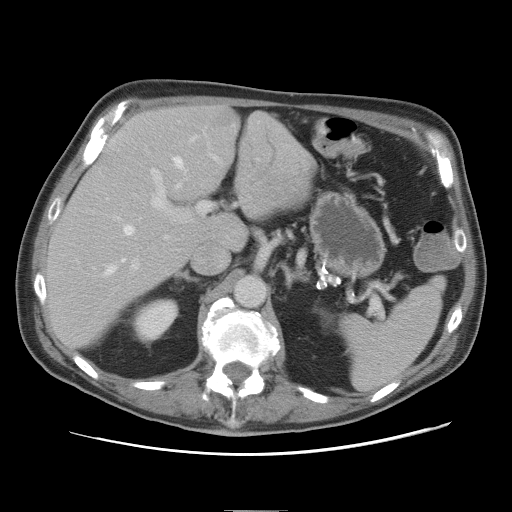
Contrast-enhanced abdominal CT, one axial slice; slice 48 of 89 in the series (ordered by position); 120 kVp; intravenous contrast given; soft-tissue window (W 400 / L 40 HU); 5 mm slice thickness; 512 × 512 image matrix, field of view 375 × 375 mm. Male patient, age 69 years. Case-level facts recorded for this patient, not image findings: diagnosis: colorectal cancer liver metastases, imaged before liver resection; multiple liver metastases: no; largest metastasis: 8.5 cm; disease in both lobes: no.
Annotated regions visible in this slice (expert manual segmentation):
- hepatic veins: bounding box (x1, y1, x2, y2) in pixels: (106, 137, 197, 274)
- liver: (42, 107, 315, 344)
- planned liver remnant (the part of the liver to remain after resection): (42, 107, 245, 344)
- portal vein (with intrahepatic branches): (131, 154, 219, 270)